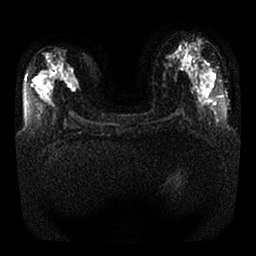
Breast MRI, one axial slice; slice 12 of 32 in the series (ordered by position); diffusion-weighted series; image 2 of 4 stored at this slice position (different b-values; order by instance number); 1.5 T; 4 mm slice thickness; 256 × 256 image matrix, field of view 350 × 350 mm. Female patient.
Annotated regions visible in this slice (expert manual segmentation):
- tumour on diffusion-weighted imaging: bounding box (x1, y1, x2, y2) in pixels: (68, 78, 78, 91)